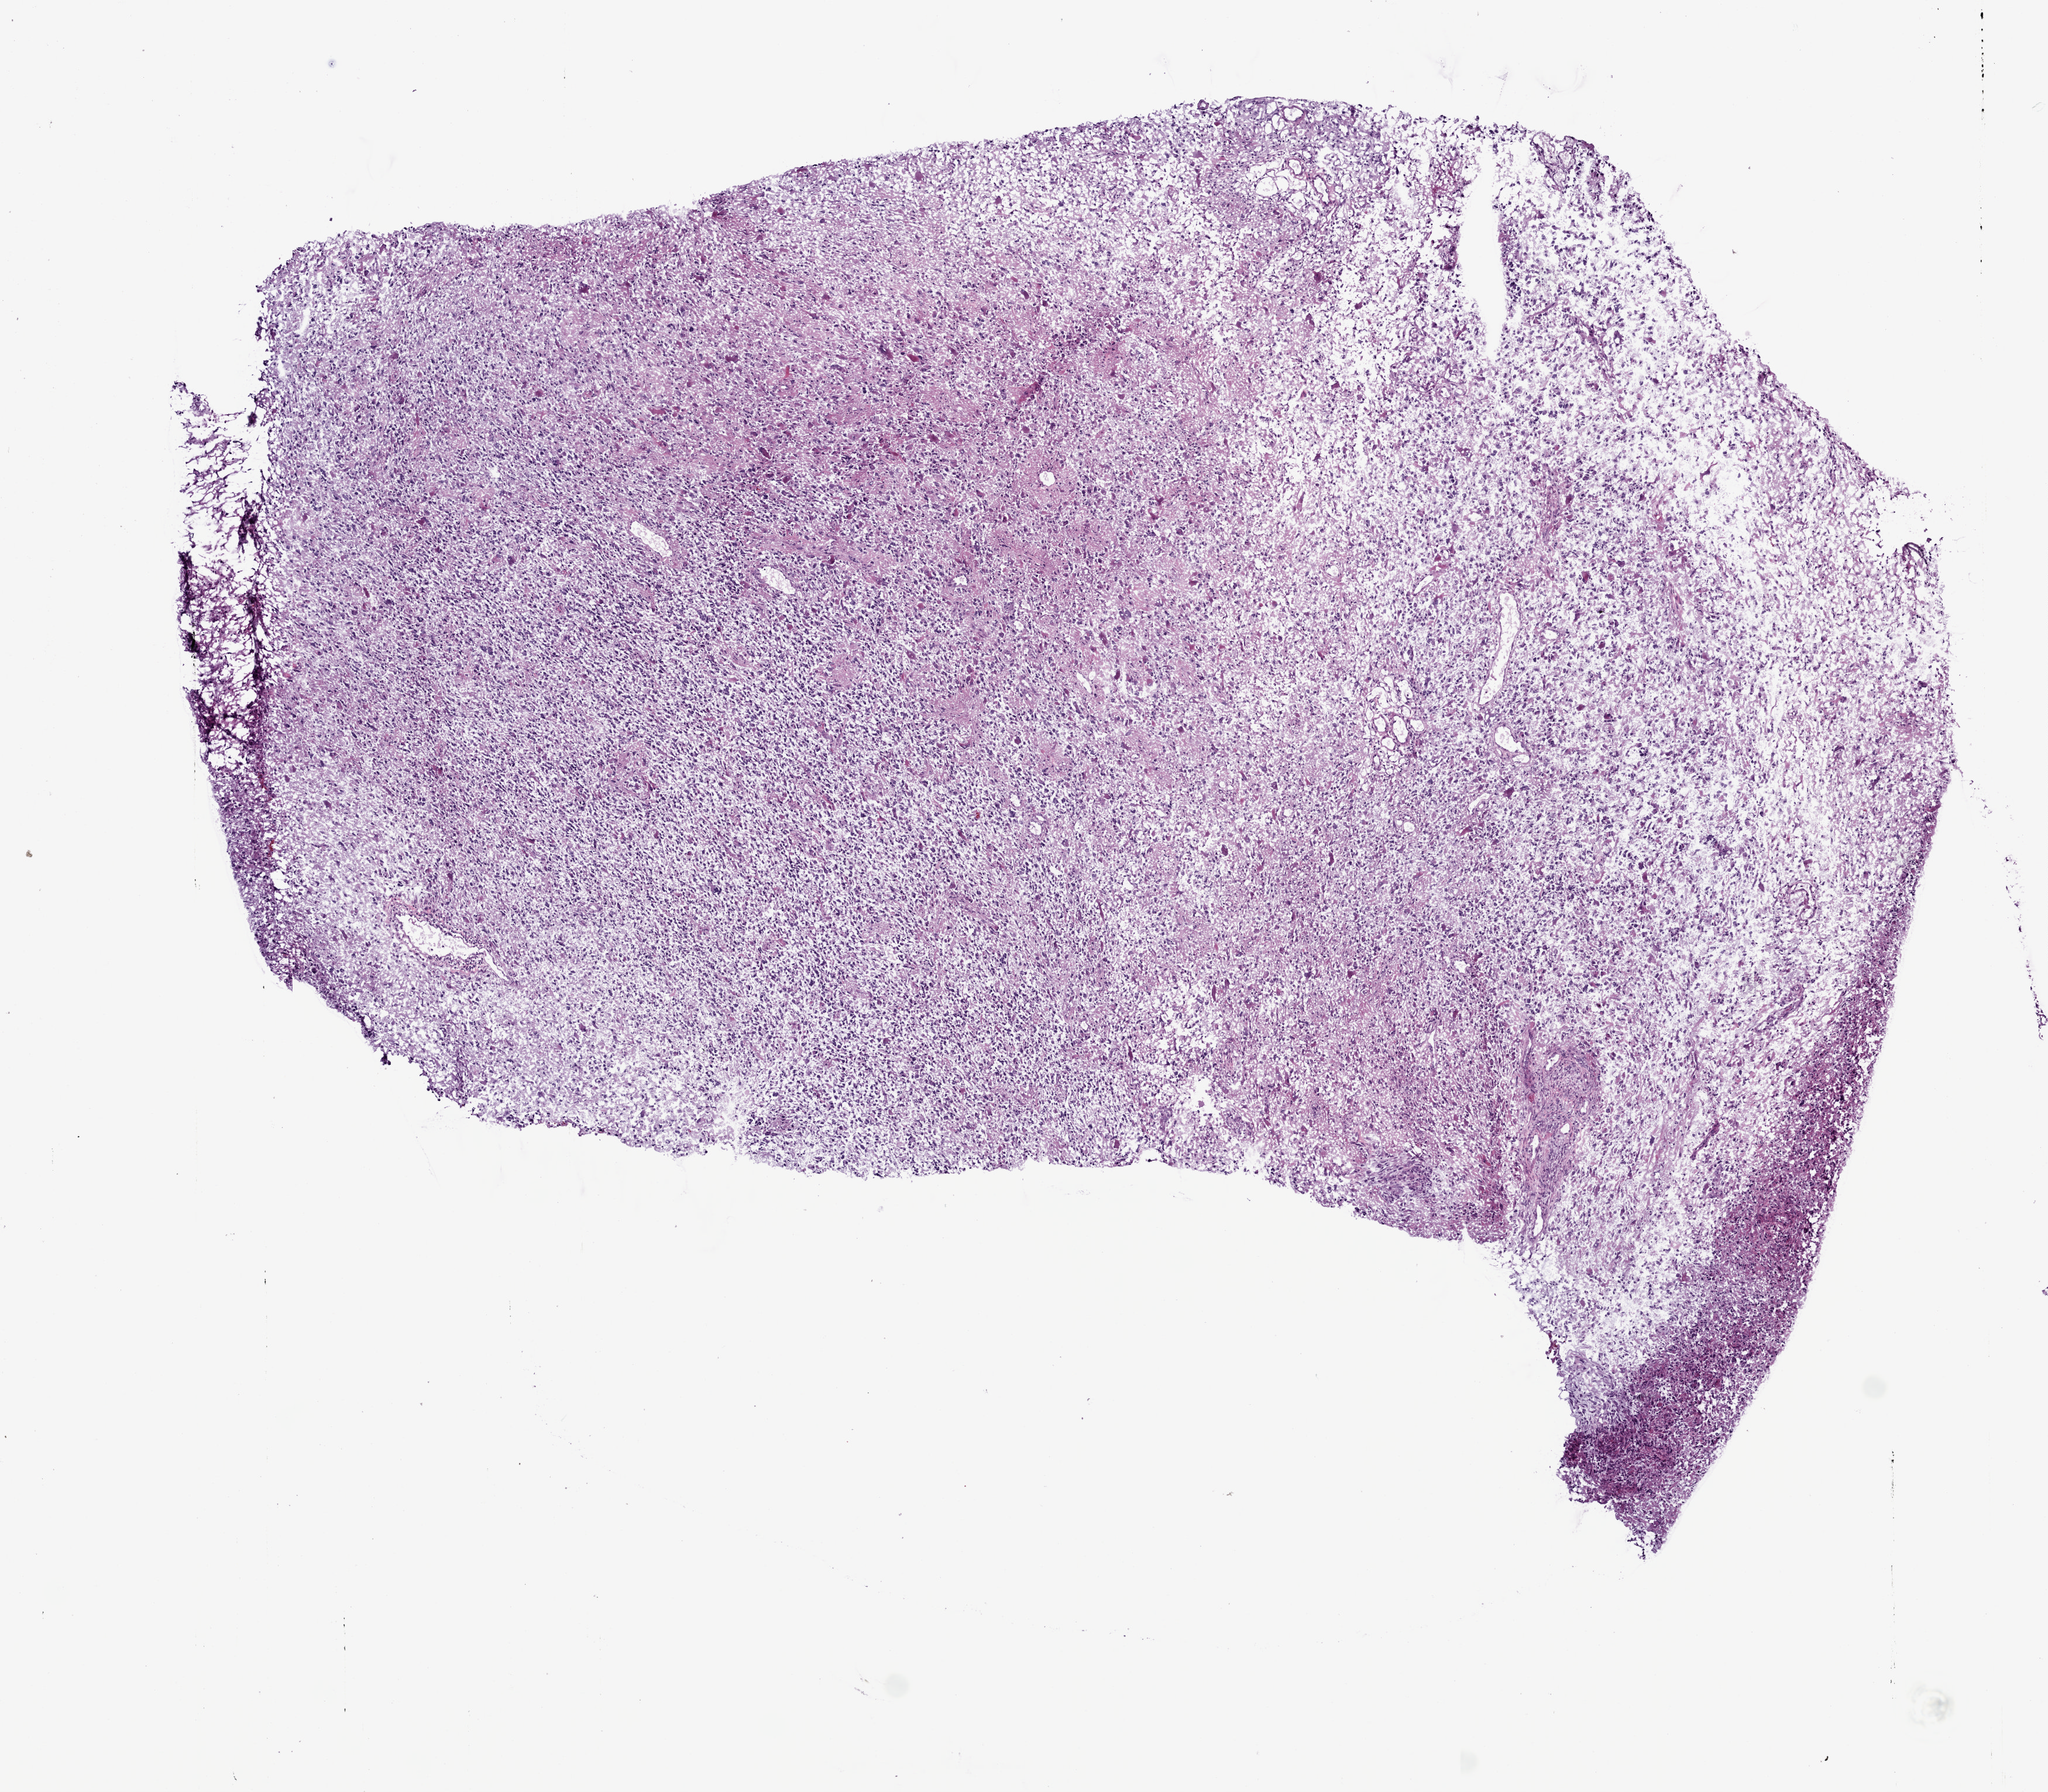
Hematoxylin and eosin (H&E) stained whole-slide image — a low-resolution overview of the entire scanned area, about 7.0 x 6.1 mm, frozen section, brain, primary tumour sample. Female, age 62 years at initial diagnosis. Slide review estimates, as recorded: tumour cells 100%, tumour nuclei 80%, normal cells 0%, stromal cells 0%, necrosis 0%.
Histologic diagnosis: Glioblastoma.